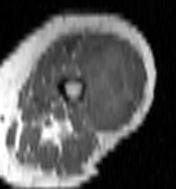
MRI of an extremity soft-tissue mass, one axial slice; position 43 of 100 along the scan axis; MR volume resampled by the dataset authors to the PET/CT grid (not the native acquisition matrix); 3.27 mm slice thickness; 176 × 189 image matrix, field of view 172 × 185 mm. Female patient. Case-level facts recorded for this patient, not image findings: histological type: undifferentiated – high grade; grade: high; site of the primary tumour: left thigh.
Annotated regions visible in this slice (expert contour drawn on MRI and transferred to this co-registered scan by the dataset authors):
- gross tumour volume including surrounding oedema: bounding box [x1, y1, x2, y2] px = [57, 39, 140, 127]
- gross tumour volume (mass): [69, 39, 138, 127]